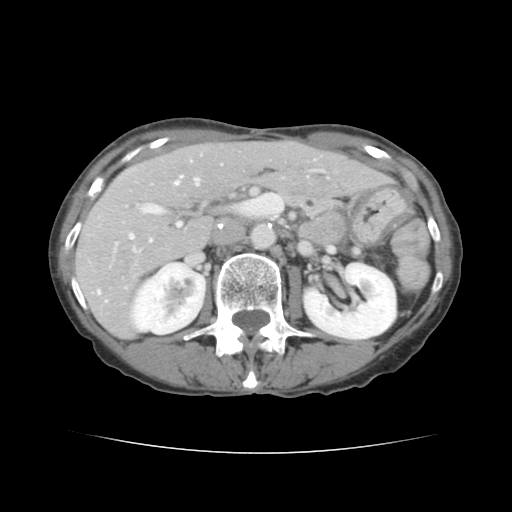
Contrast-enhanced abdominal CT, one axial slice. Position 71 of 136 along the scan axis. Intravenous contrast given. Soft-tissue window (W 400 / L 40 HU). 2.5 mm slice thickness. 512 × 512 image matrix. Female patient, age 77 years. From the clinical record (not read from this slice): diagnosis: colorectal cancer liver metastases, imaged before liver resection; multiple liver metastases: yes; largest metastasis: 3 cm.
Structures marked on this image (expert manual segmentation):
- hepatic veins: bounding box (x1, y1, x2, y2) in pixels: (129, 176, 199, 238)
- liver: (76, 142, 386, 337)
- planned liver remnant (the part of the liver to remain after resection): (158, 143, 387, 200)
- portal vein (with intrahepatic branches): (98, 206, 181, 293)